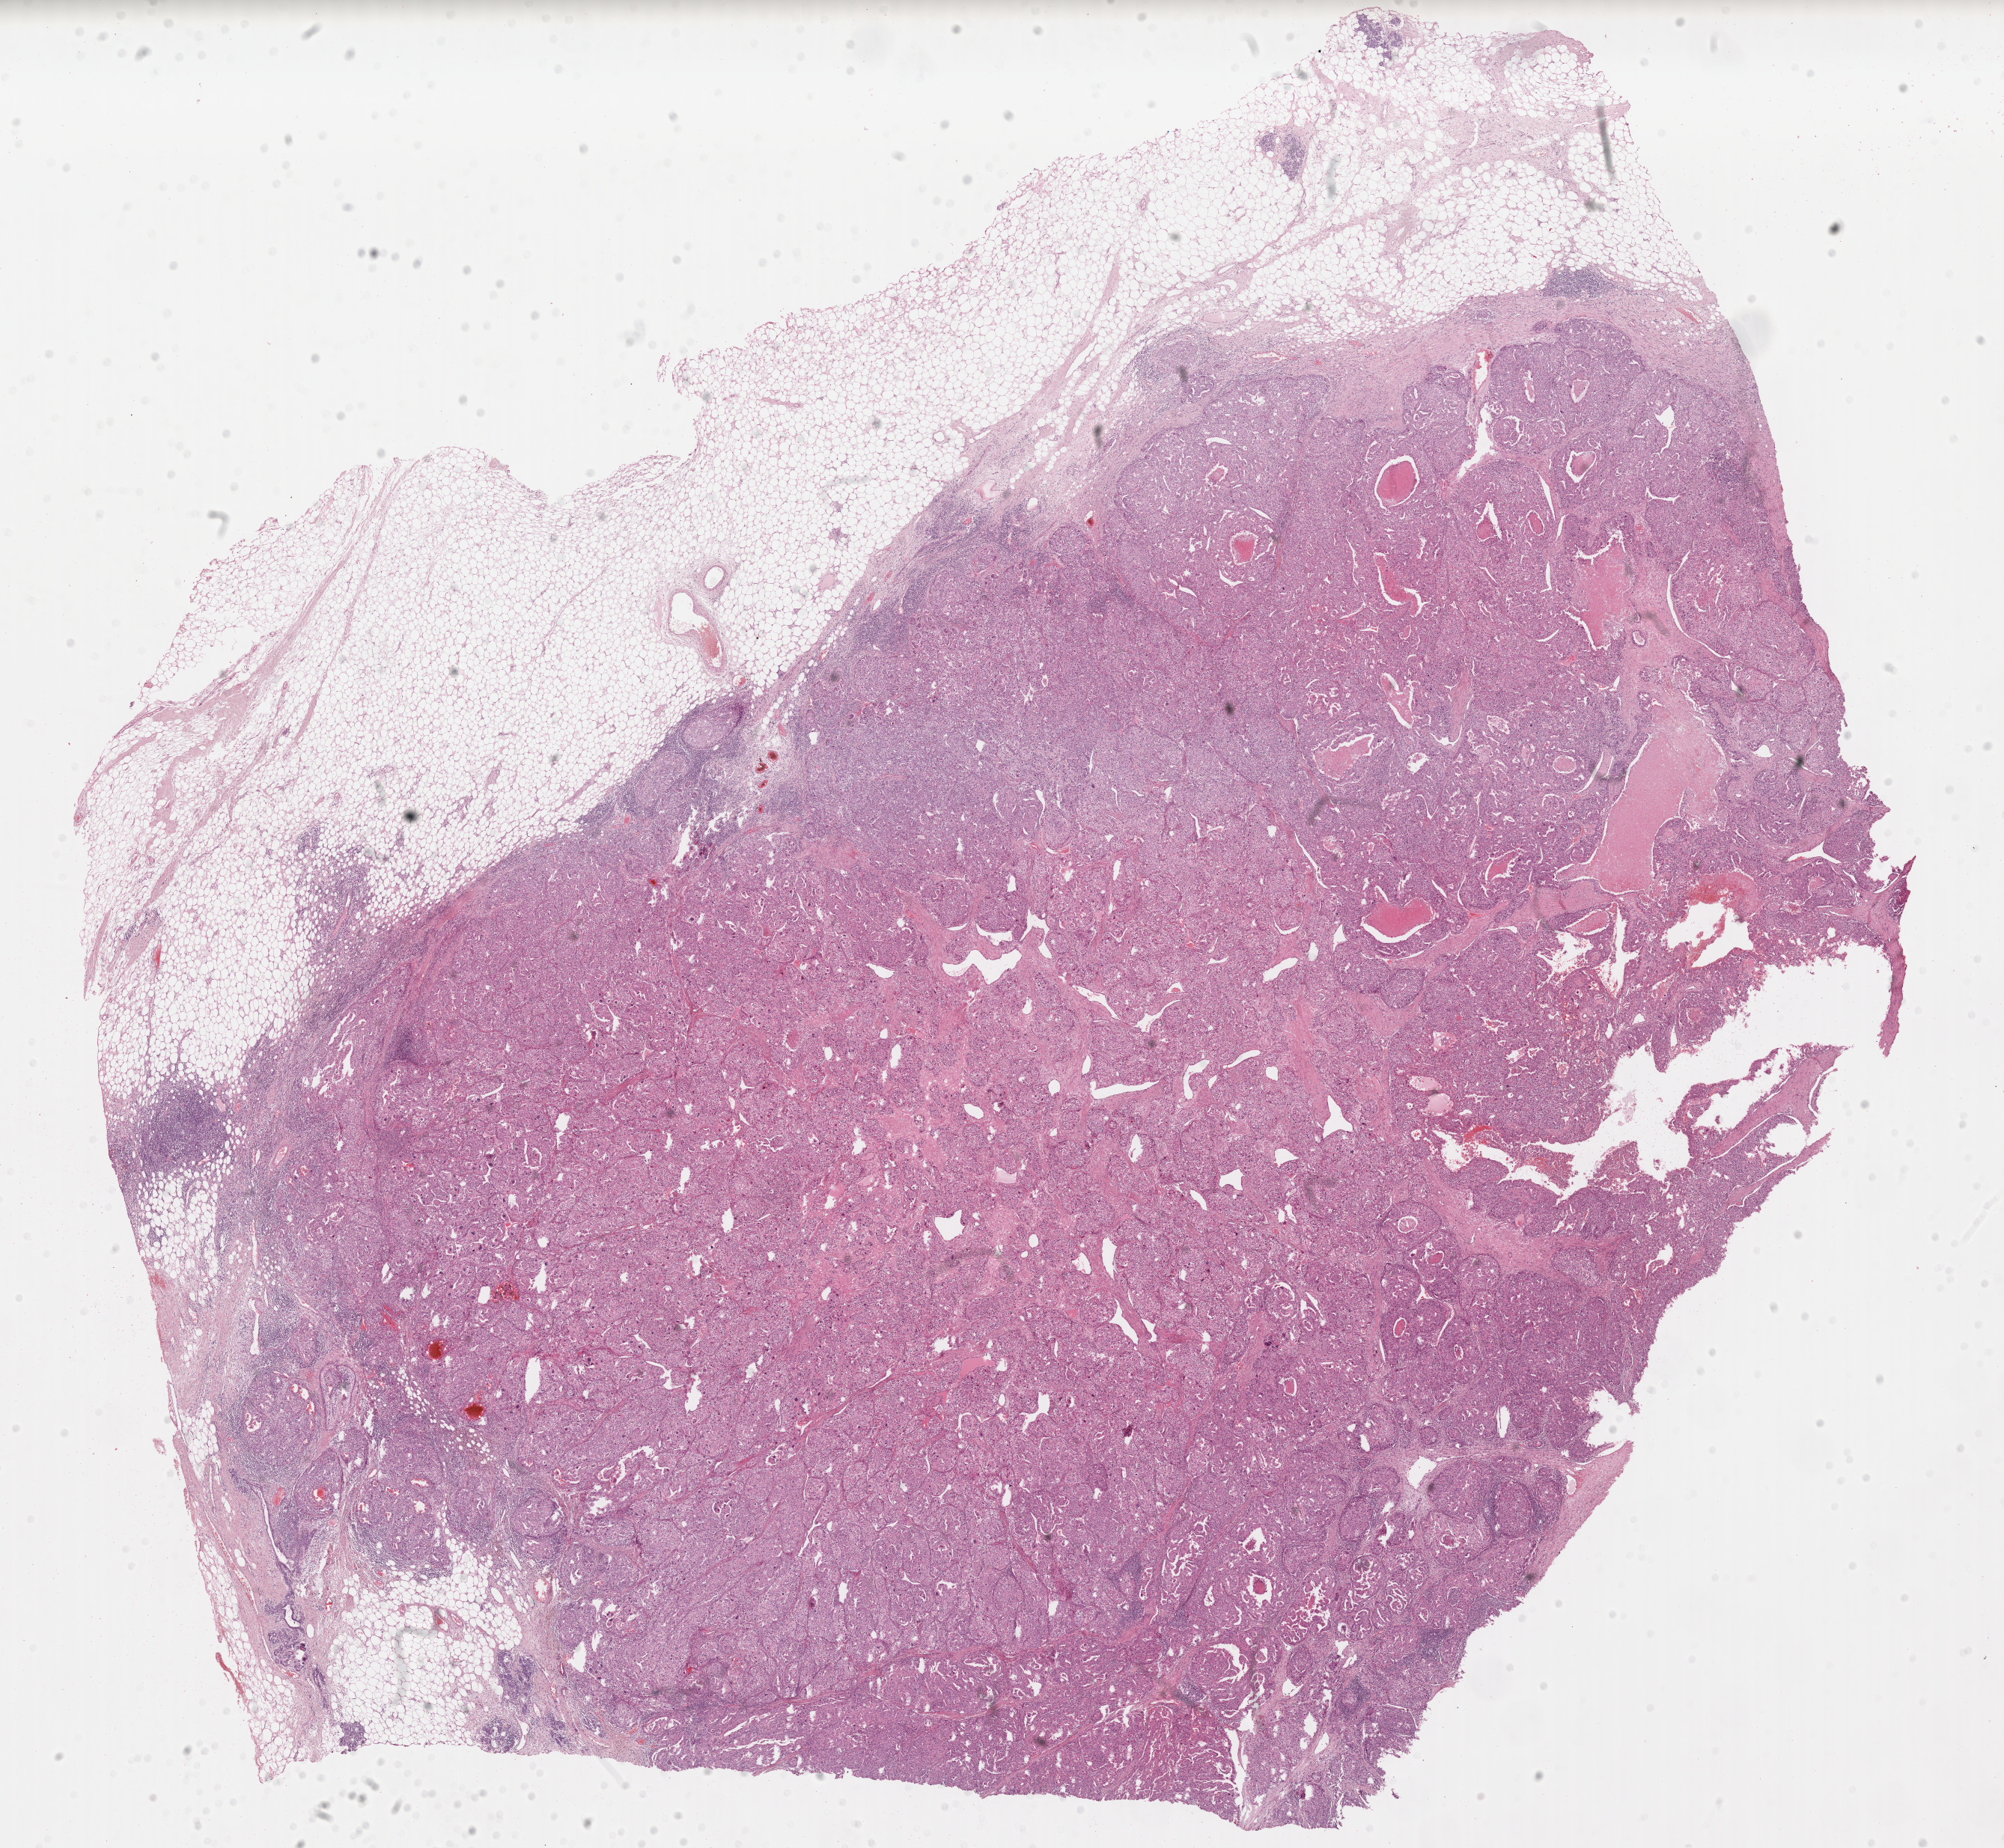
Digitized H&E-stained tissue section (whole slide), low-resolution overview of the scanned area, about 21.1 x 19.5 mm, formalin-fixed paraffin-embedded (FFPE) diagnostic section, breast, primary tumour sample. Female, age 53 years at initial diagnosis.
AJCC pathologic stage: IIA (7th edition). Pathologic diagnosis: Infiltrating duct carcinoma, NOS. Lymph nodes positive (case pathology): 0 of 1 examined.